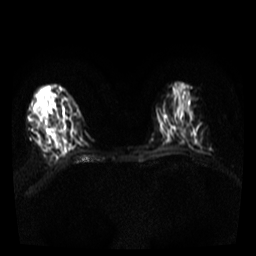
Breast MRI, one axial slice; slice 13 of 36 in the series (ordered by position); diffusion-weighted series; image 2 of 4 stored at this slice position (different b-values; order by instance number); 3 T; 5 mm slice thickness; 256 × 256 image matrix, field of view 300 × 300 mm. Female patient.
Annotated regions visible in this slice (expert manual segmentation):
- tumour on diffusion-weighted imaging: bounding box (x1, y1, x2, y2) in pixels: (35, 105, 44, 114)